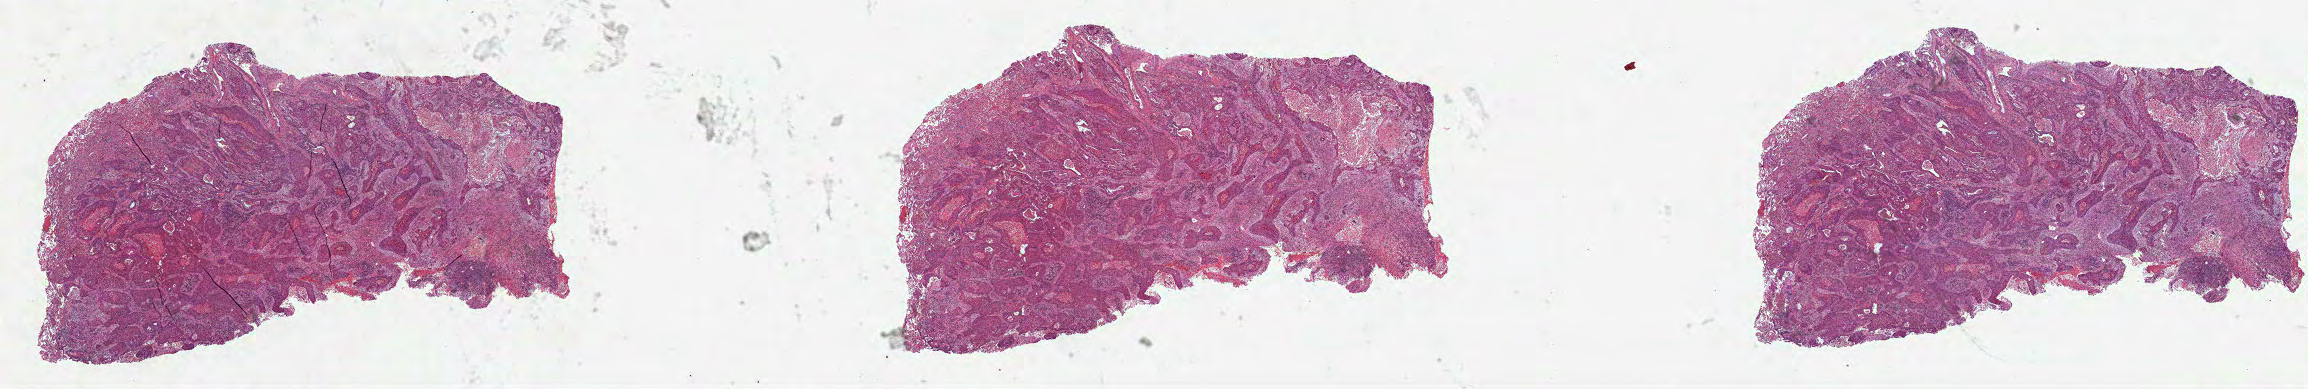
Digitized Hematoxylin and eosin (H&E) stained tissue section (whole slide), whole scanned area (about 37.2 x 6.3 mm) shown as a low-resolution overview. FFPE section. Sample: primary tumour, lung. Patient: female, age at initial diagnosis 59 years.
• AJCC pathologic stage: IB (7th edition)
• laterality: left
• diagnosis: Squamous cell carcinoma, NOS (upper lobe, lung)